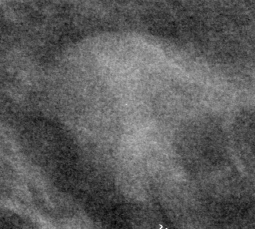
Crop from a digitized film mammogram around one marked abnormality; right breast; CC view.
Finding: mass, shape lobulated, margins circumscribed / ill defined; BI-RADS assessment category 4; pathology result (as recorded, not read from the image): benign.